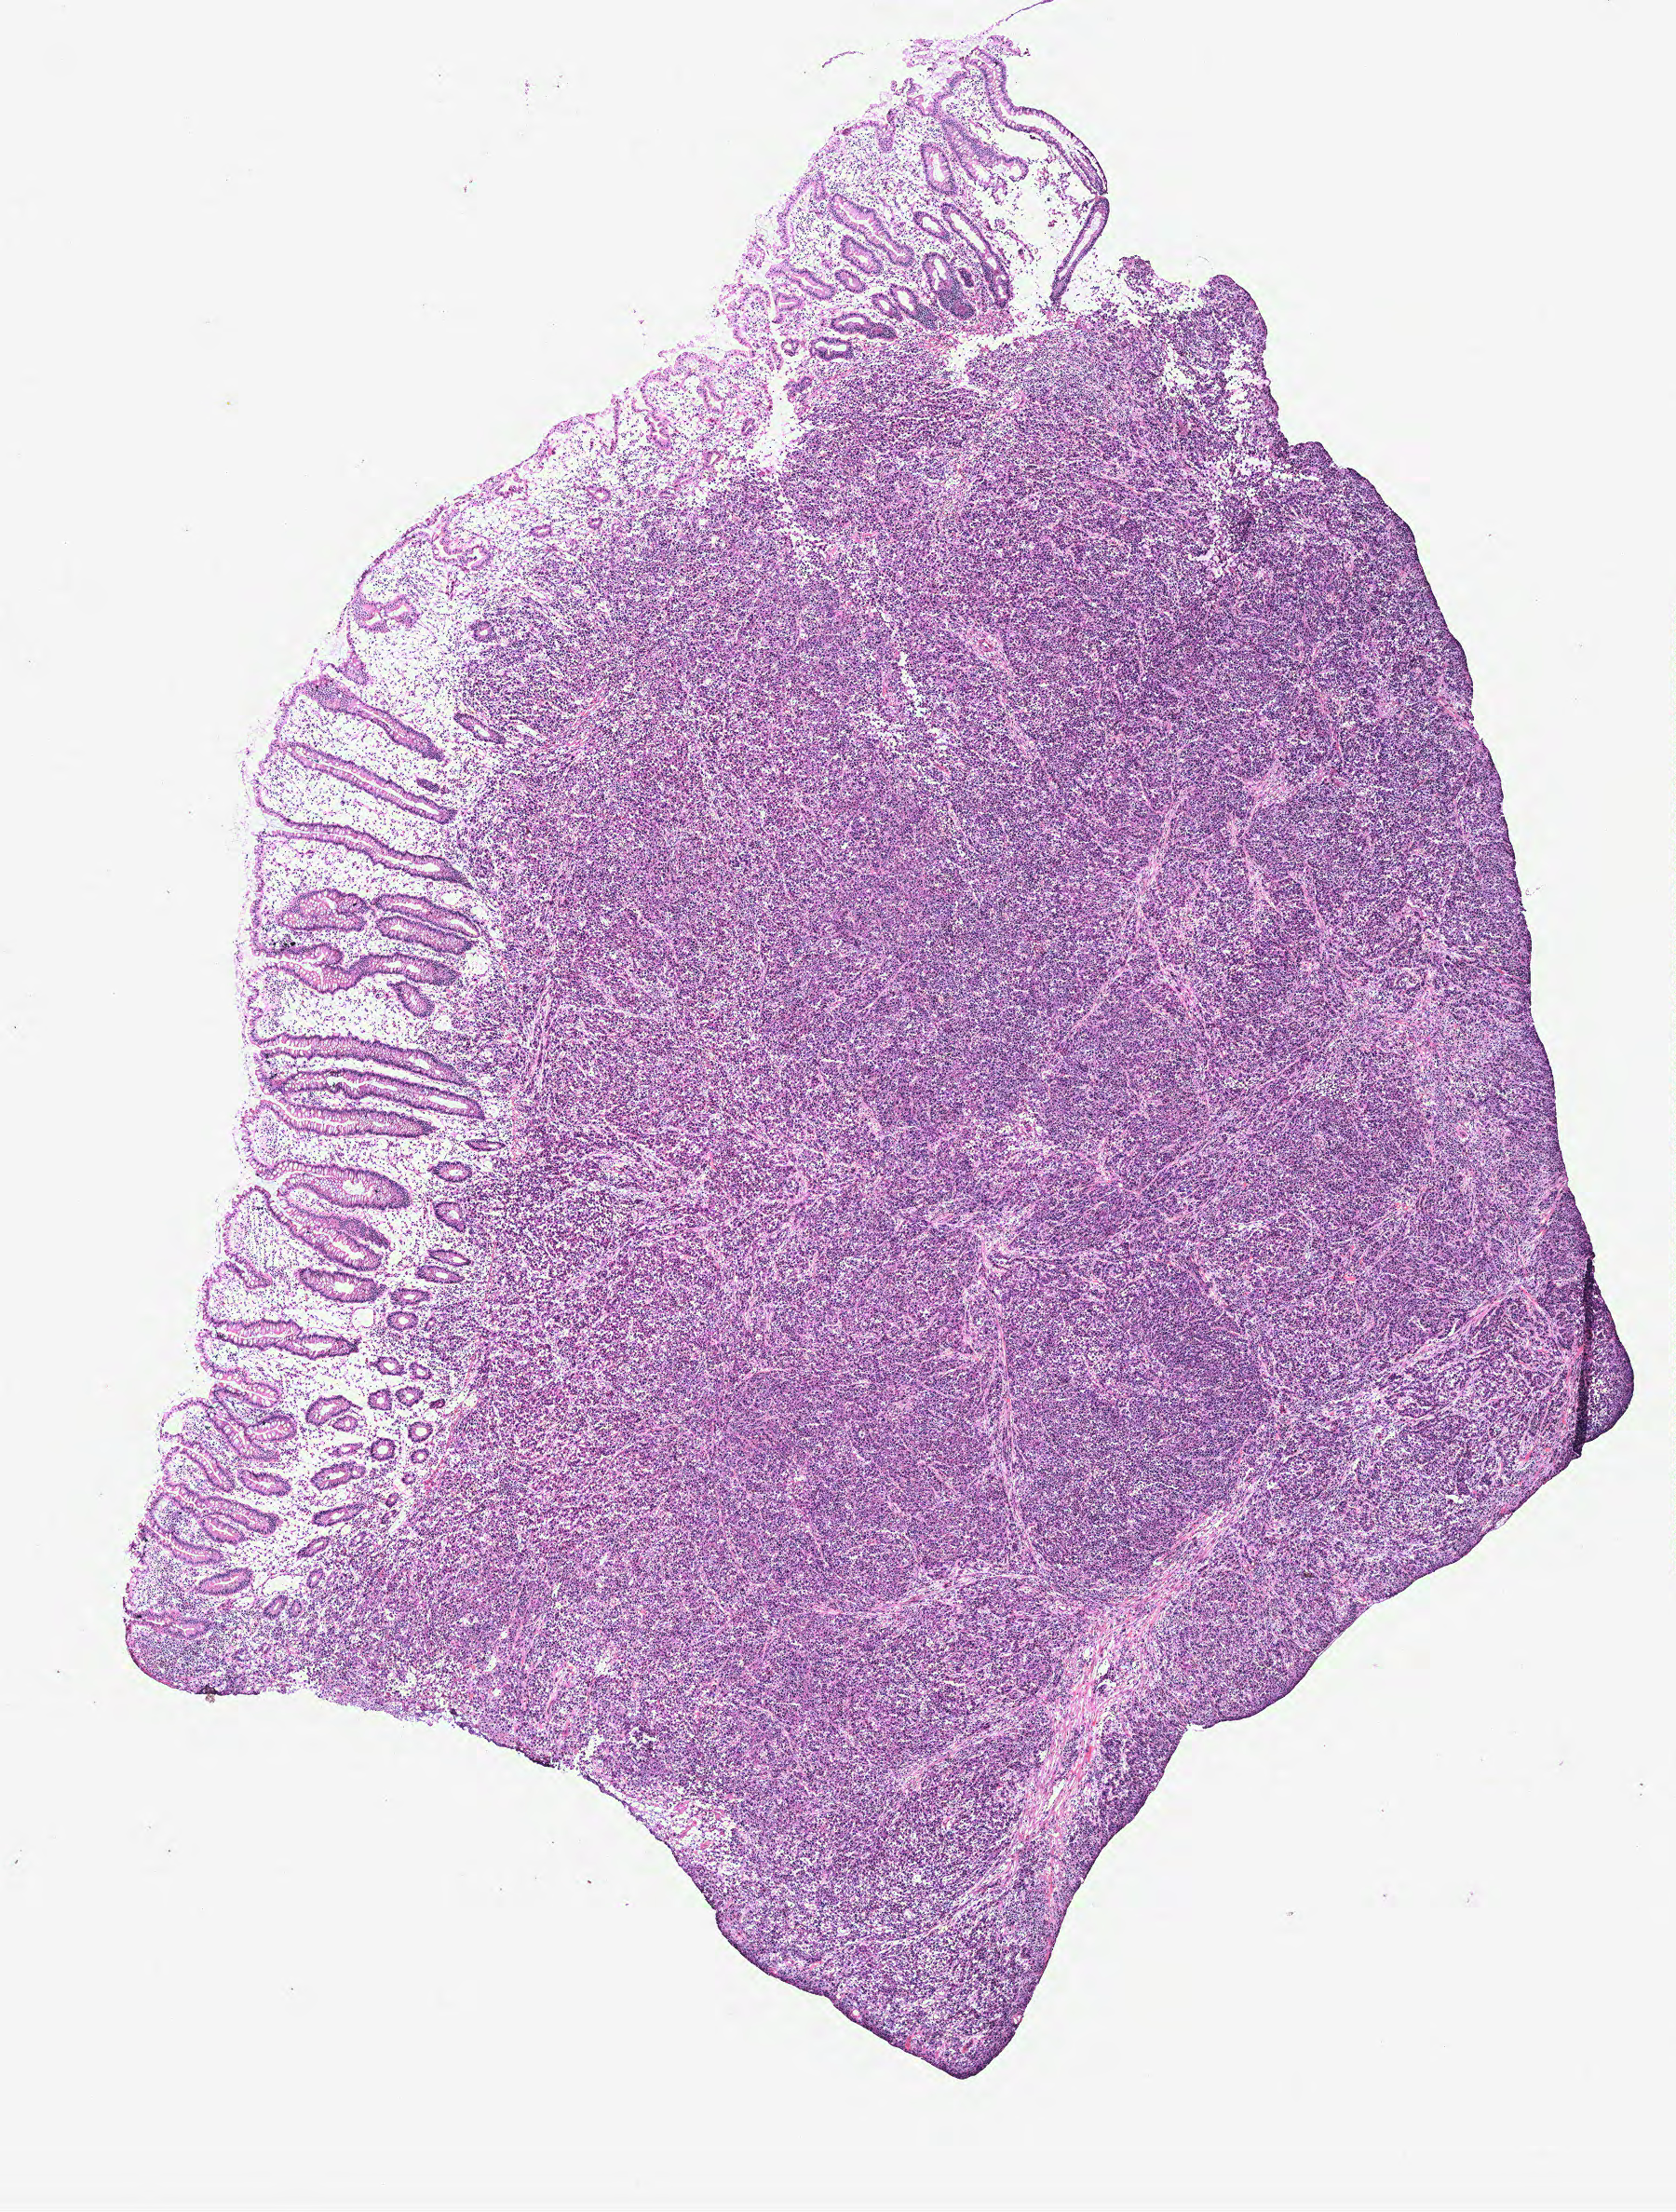
Whole-slide histology image, H&E — low-resolution overview of the scanned area, about 7.2 x 9.5 mm (slide scanned at 40x). Colon, tissue type not recorded.
Patient diagnosis (cohort enrolment): colon cancer (colon).